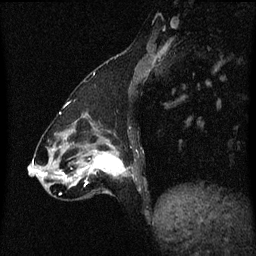
Breast MRI (dynamic contrast-enhanced), one sagittal slice. Dynamic contrast-enhanced series, image 2 of 3 at this slice position (ordered by acquisition). 1.5 T. TE 4.2 ms, TR 8.4 ms. 2 mm slice thickness. 256 × 256 image matrix, field of view 200 × 200 mm. Female patient, age 47 years.
Structures marked on this image (semi-automatically segmented with operator editing):
- analysis volume of interest (the breast-tissue region the enhancement analysis was run in; not a lesion): bounding box (x1, y1, x2, y2) in pixels: (81, 140, 135, 195)
- tumour enhancement mask (voxels above the 70 % enhancement threshold inside the analysis volume of interest): (81, 150, 126, 185)